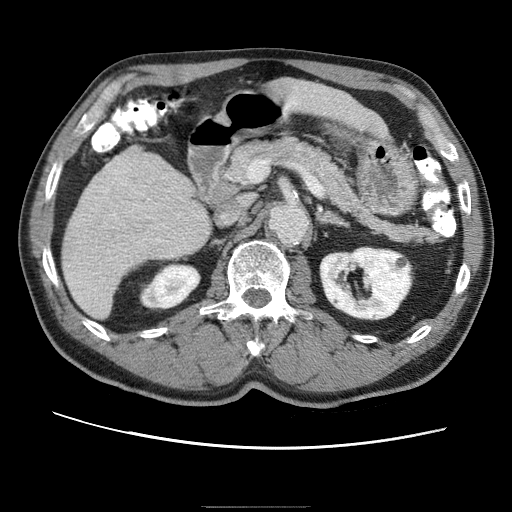
Contrast-enhanced abdominal CT (liver protocol), one axial slice. Slice 20 of 75 in the series (ordered by position). 120 kVp. One of 2 acquisitions stored at this slice position. Soft-tissue window (W 400 / L 40 HU). 2.5 mm slice thickness. 512 × 512 image matrix. Case-level facts recorded for this patient, not image findings: diagnosis: hepatocellular carcinoma (patient treated with transarterial chemoembolisation; whether this scan precedes or follows treatment is not stated here); TNM stage (as recorded): Stage-II; Child-Pugh class: A.
Annotated regions visible in this slice (semi-automatically segmented with operator editing):
- liver parenchyma outside the tumour (the mass and vessels are separate outlines, so this box may not span the whole liver): box from (x=62, y=150) to (x=204, y=316) px
- liver vessels: (x=97, y=164)–(x=113, y=186)